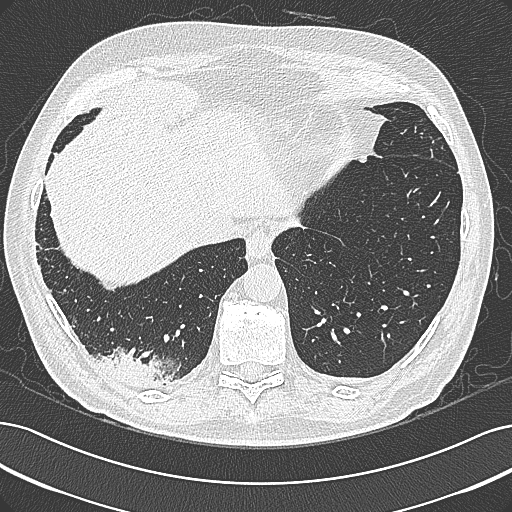
Axial slice from a low-dose chest CT screening exam; baseline screening round; lung window (W 1500 / L -600 HU); 1 mm slice thickness; lung (sharp) reconstruction kernel (B80f); 120 kVp; slice 235 of 355 in the series; 512 × 512 image matrix, field of view 362 × 362 mm. Male participant, aged 68 years at enrolment. Former smoker at enrolment.
Expert reader's lesion annotation, bounding box <97,340,186,401> (left, top, right, bottom; pixels). Screening reader's record for this exam: no non-calcified nodule ≥4 mm recorded. Official screen result: negative screen, significant abnormalities not suspicious for lung cancer. Lung cancer was diagnosed 154 days after this screen: mucinous adenocarcinoma, right lower lobe, well differentiated (G1), stage IB (AJCC 6th edition), 50 mm at pathology.